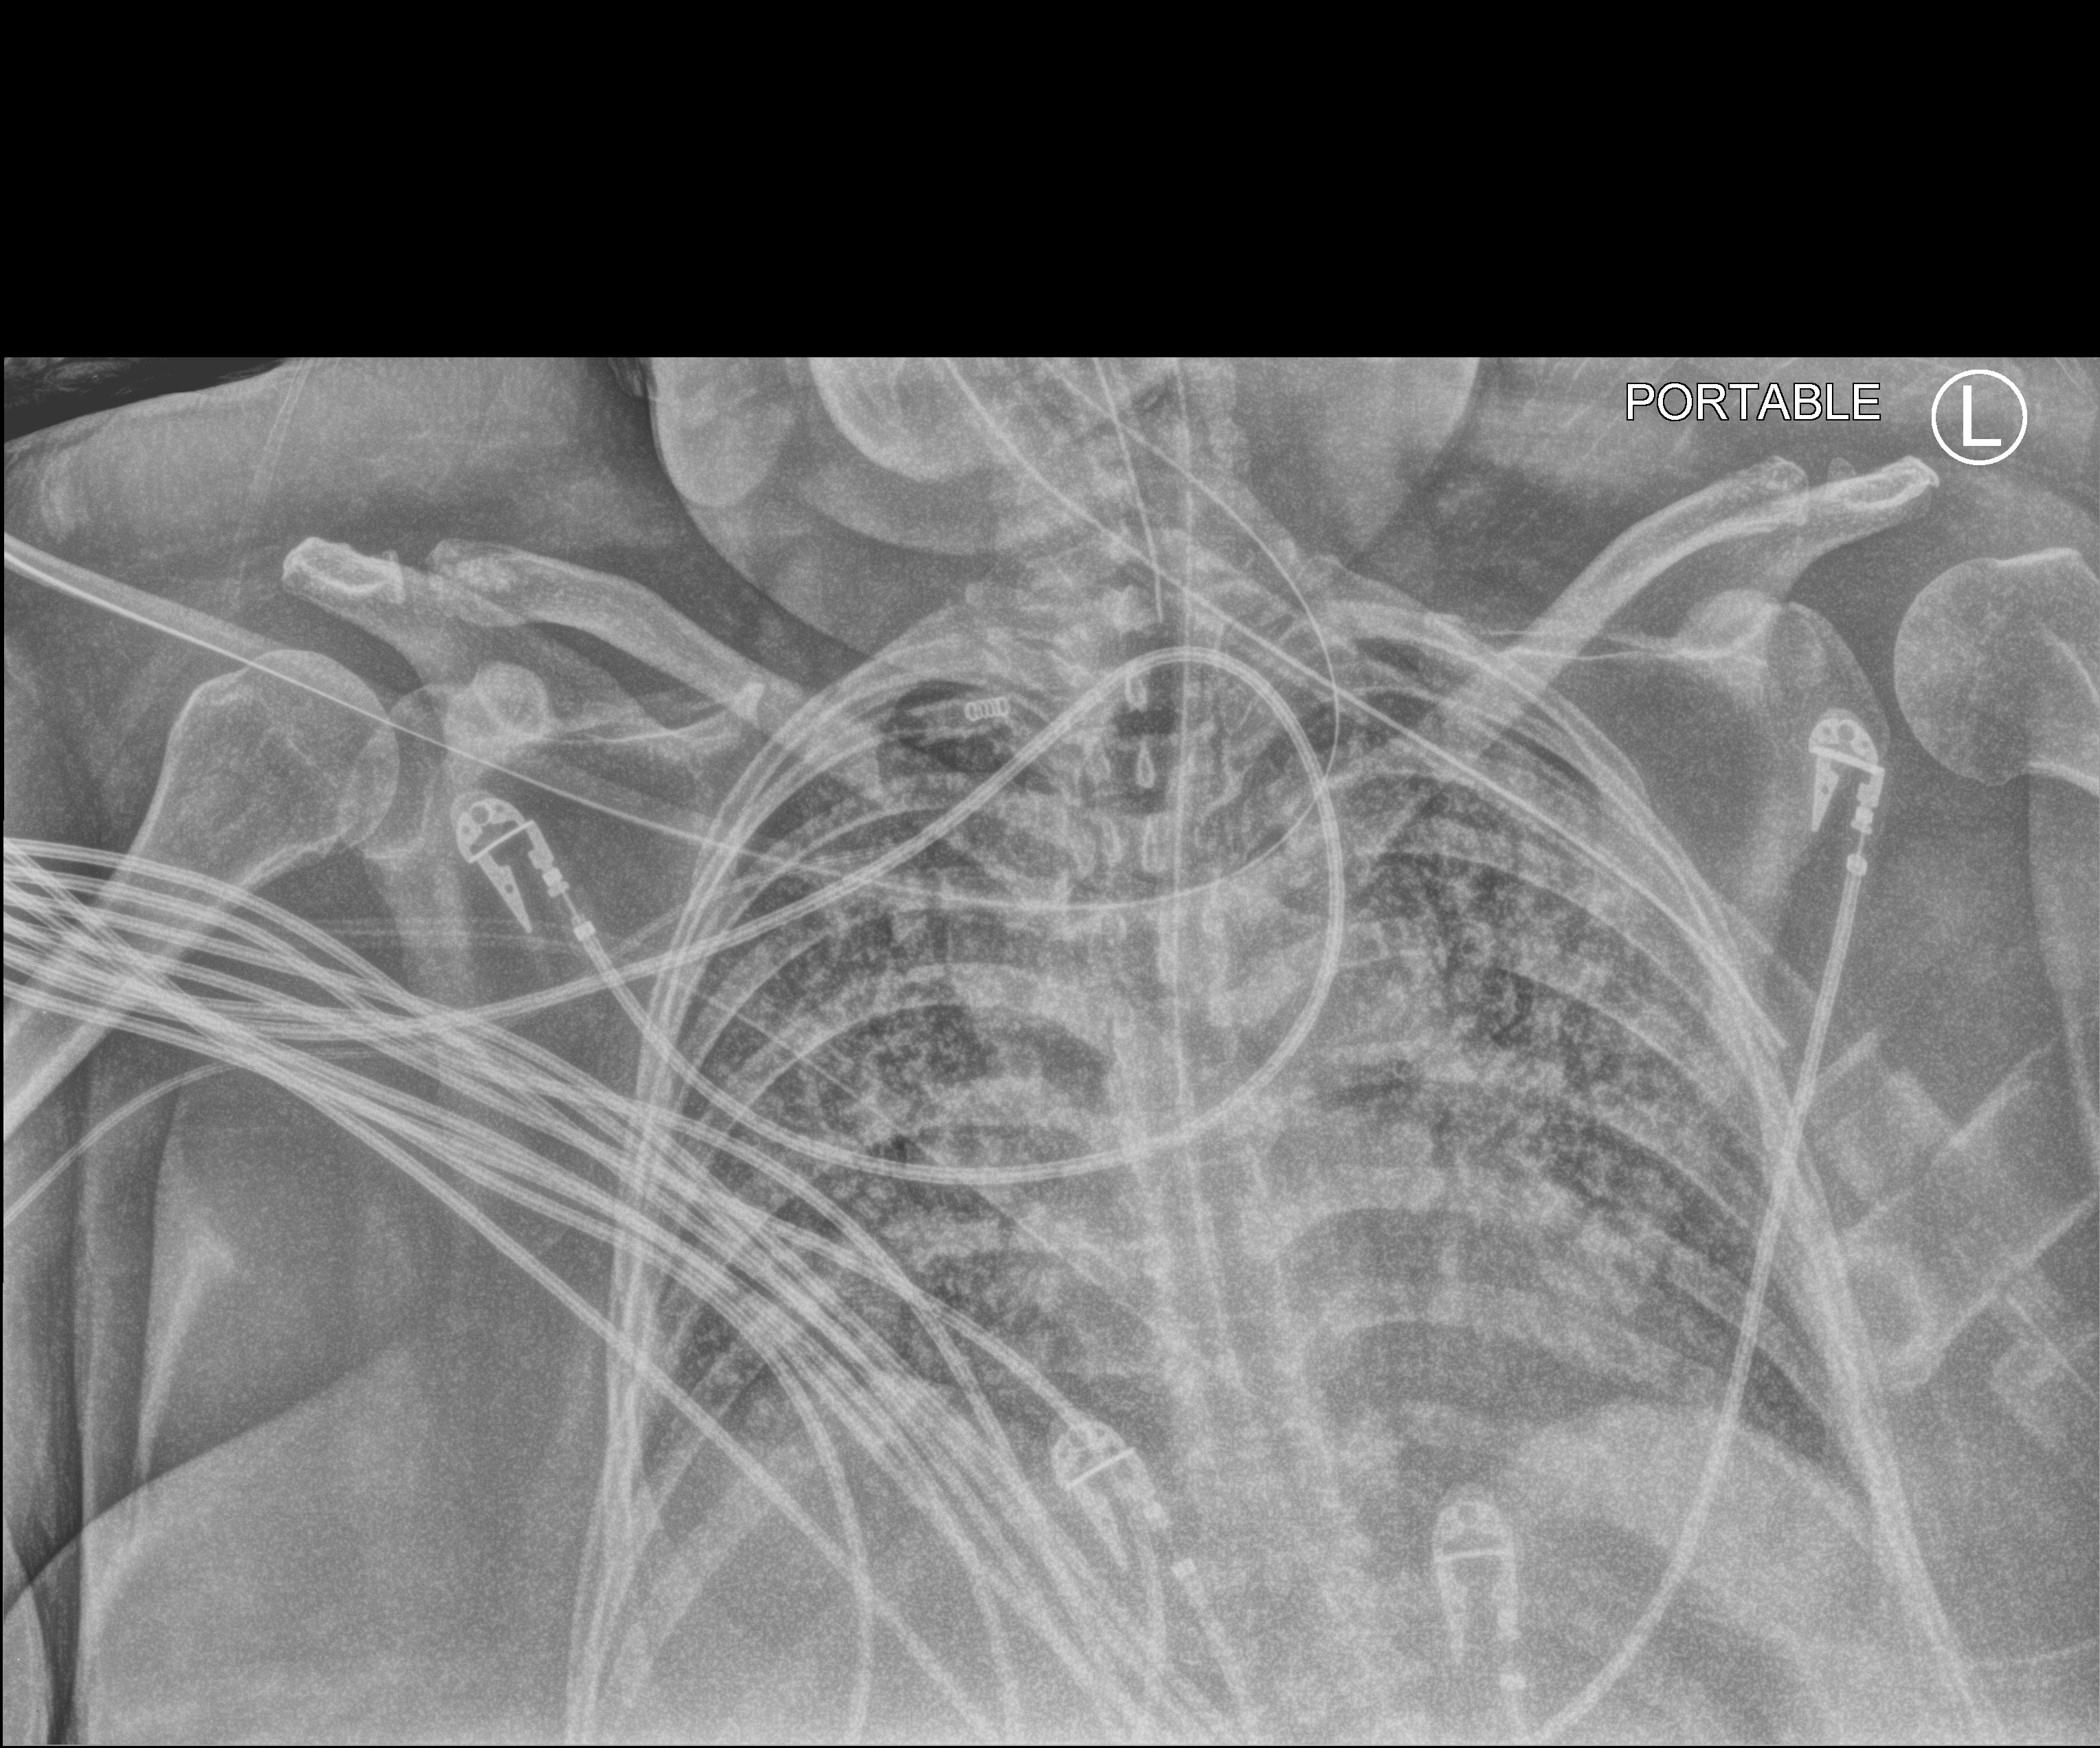
Bedside chest radiograph (computed radiography); anteroposterior (AP) projection. Patient hospitalised with COVID-19; female, aged 18–59 years.
Admission-level facts for this patient (not findings on this image; timing relative to this image not recorded): other chronic lung disease (admission record): no.